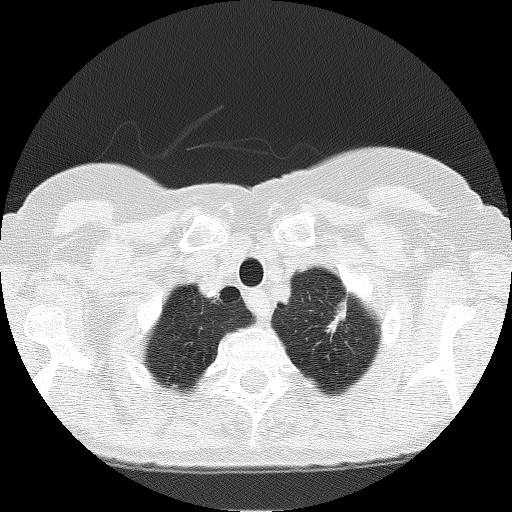
Axial slice from a low-dose chest CT screening exam, first (baseline) screen, lung window (W 1500 / L -600 HU), 2 mm slice thickness, lung (sharp) reconstruction kernel (FC51). Female participant, aged 66 years at enrolment. Current smoker at enrolment.
Expert-annotated lung lesion, bounding box (x1, y1, x2, y2) in pixels: (312, 289, 366, 342). The screening reader recorded 3 non-calcified nodules or masses ≥4 mm on this exam; which of them this box marks is not recorded. Official screen result: positive, change unspecified: nodule(s) >= 4 mm or enlarging nodule(s), mass(es), or other non-specific abnormalities suspicious for lung cancer.